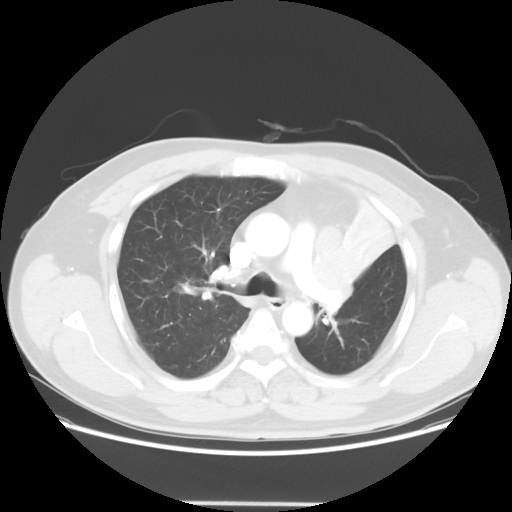
Chest CT, one axial slice; position 41 of 62 along the scan axis; 120 kVp; lung window (W 1500 / L -600 HU); 5 mm slice thickness; 512 × 512 image matrix, field of view 403 × 403 mm. Patient: male, 49 years. From the clinical record (not read from this slice): clinical TNM (as recorded): T3 N3 M1c.
Annotated regions visible in this slice (rectangle marked by the reading radiologist):
- lung tumour (recorded histology: squamous cell carcinoma): bounding box (x1, y1, x2, y2) in pixels: (306, 221, 360, 316)